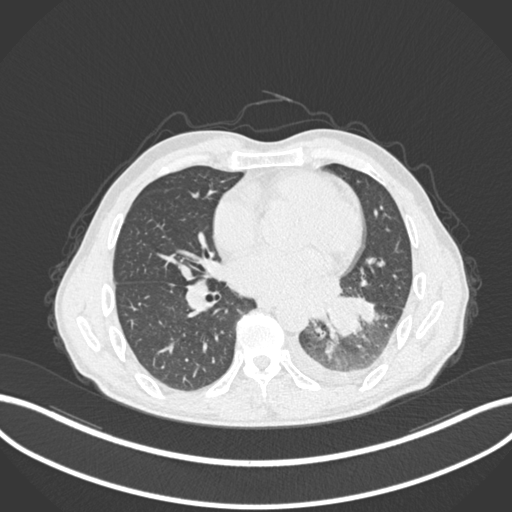
Chest CT, one axial slice; position 107 of 222 along the scan axis; reconstruction kernel B30f; 120 kVp; lung window (W 1500 / L -600 HU); 512 × 512 image matrix. Male patient, age 47 years. Case-level facts recorded for this patient, not image findings: clinical TNM (as recorded): T3 N1 M1c.
Outlined on this slice (rectangle marked by the reading radiologist):
- lung tumour (recorded histology: small cell carcinoma): bounding box (x1, y1, x2, y2) in pixels: (326, 294, 361, 341)